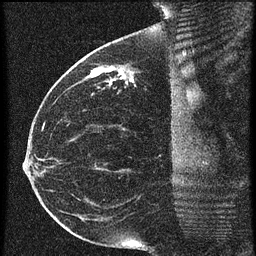
Breast MRI (dynamic contrast-enhanced), one sagittal slice. Slice 27 of 60 in the series (ordered by position). 3 images stored at this slice position (order not interpretable as contrast timing). 1.5 T. TE 4.2 ms, TR 20.4 ms. 1.5 mm slice thickness. 256 × 256 image matrix, field of view 200 × 200 mm. Patient: female, 35 years. Case-level facts recorded for this patient, not image findings: setting: breast cancer imaged before/during neoadjuvant chemotherapy; receptor status: HR-positive, HER2-negative.
Annotated regions visible in this slice (semi-automatic segmentation, software-assisted and operator-edited):
- analysis volume of interest (the breast-tissue region the enhancement analysis was run in; not a lesion): bounding box <84,50,179,97> (left, top, right, bottom; pixels)
- tumour enhancement mask (voxels above the 90 % enhancement threshold inside the analysis volume of interest): <90,68,133,85>